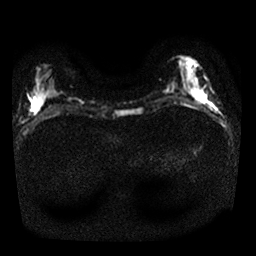
Breast MRI, one axial slice; position 7 of 25 along the scan axis; diffusion-weighted series; image 2 of 4 stored at this slice position (different b-values; order by instance number); 1.5 T; 4 mm slice thickness; 256 × 256 image matrix, field of view 320 × 320 mm. Female patient.
Outlined on this slice (manually delineated by an expert):
- tumour on diffusion-weighted imaging: bounding box [x1, y1, x2, y2] px = [203, 96, 206, 101]